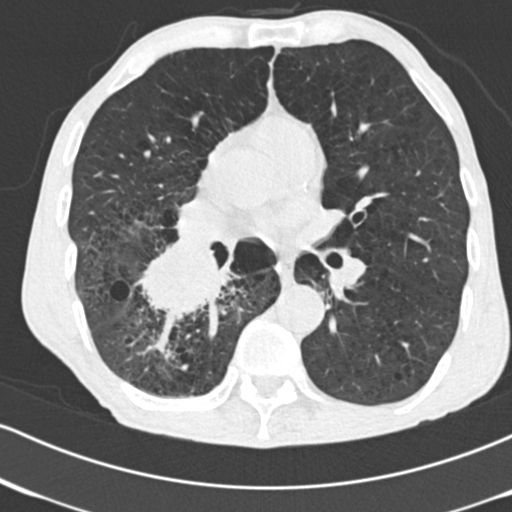
Low-dose screening chest CT, one axial slice. 120 kVp. Lung window (W 1500 / L -600 HU). 512 × 512 image matrix, field of view 316 × 316 mm.
Annotated regions visible in this slice (outlined manually by an expert reader):
- lesion 1 (tumor, lower lobe of right lung): box from (x=141, y=242) to (x=230, y=318) px